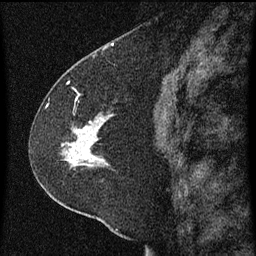
Breast MRI (dynamic contrast-enhanced), one sagittal slice; position 33 of 60 along the scan axis; dynamic contrast-enhanced series, image 2 of 3 at this slice position (ordered by acquisition); 1.5 T; TE 4.2 ms, TR 8 ms; 256 × 256 image matrix, field of view 180 × 180 mm. Female patient, age 47 years.
Annotated regions visible in this slice (semi-automatically segmented with operator editing):
- analysis volume of interest (the breast-tissue region the enhancement analysis was run in; not a lesion): box from (x=36, y=96) to (x=133, y=213) px
- tumour enhancement mask (voxels above the 70 % enhancement threshold inside the analysis volume of interest): (x=68, y=118)–(x=101, y=167)